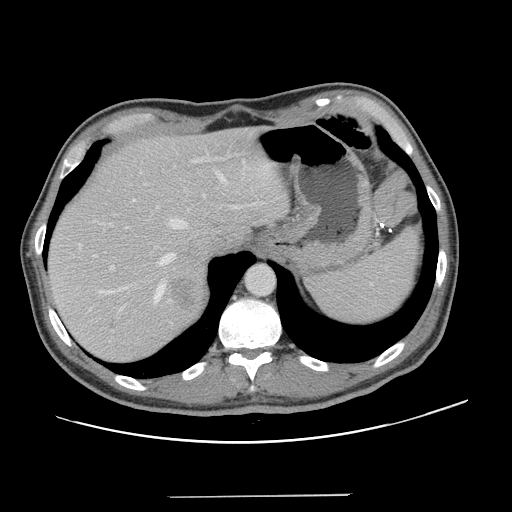
Contrast-enhanced abdominal CT, one axial slice; slice 103 of 131 in the series (ordered by position); 120 kVp; intravenous contrast given; soft-tissue window (W 400 / L 40 HU); 2.5 mm slice thickness; 512 × 512 image matrix, field of view 403 × 403 mm. Male patient, age 60 years. Case-level facts recorded for this patient, not image findings: diagnosis: colorectal cancer liver metastases, imaged before liver resection; multiple liver metastases: no; largest metastasis: 2.5 cm; disease in both lobes: no.
Structures marked on this image (outlined manually by an expert reader):
- hepatic veins: bounding box (x1, y1, x2, y2) in pixels: (99, 170, 225, 311)
- liver: (47, 128, 287, 362)
- planned liver remnant (the part of the liver to remain after resection): (47, 128, 287, 351)
- portal vein (with intrahepatic branches): (92, 156, 260, 271)
- liver metastasis: (169, 277, 202, 312)